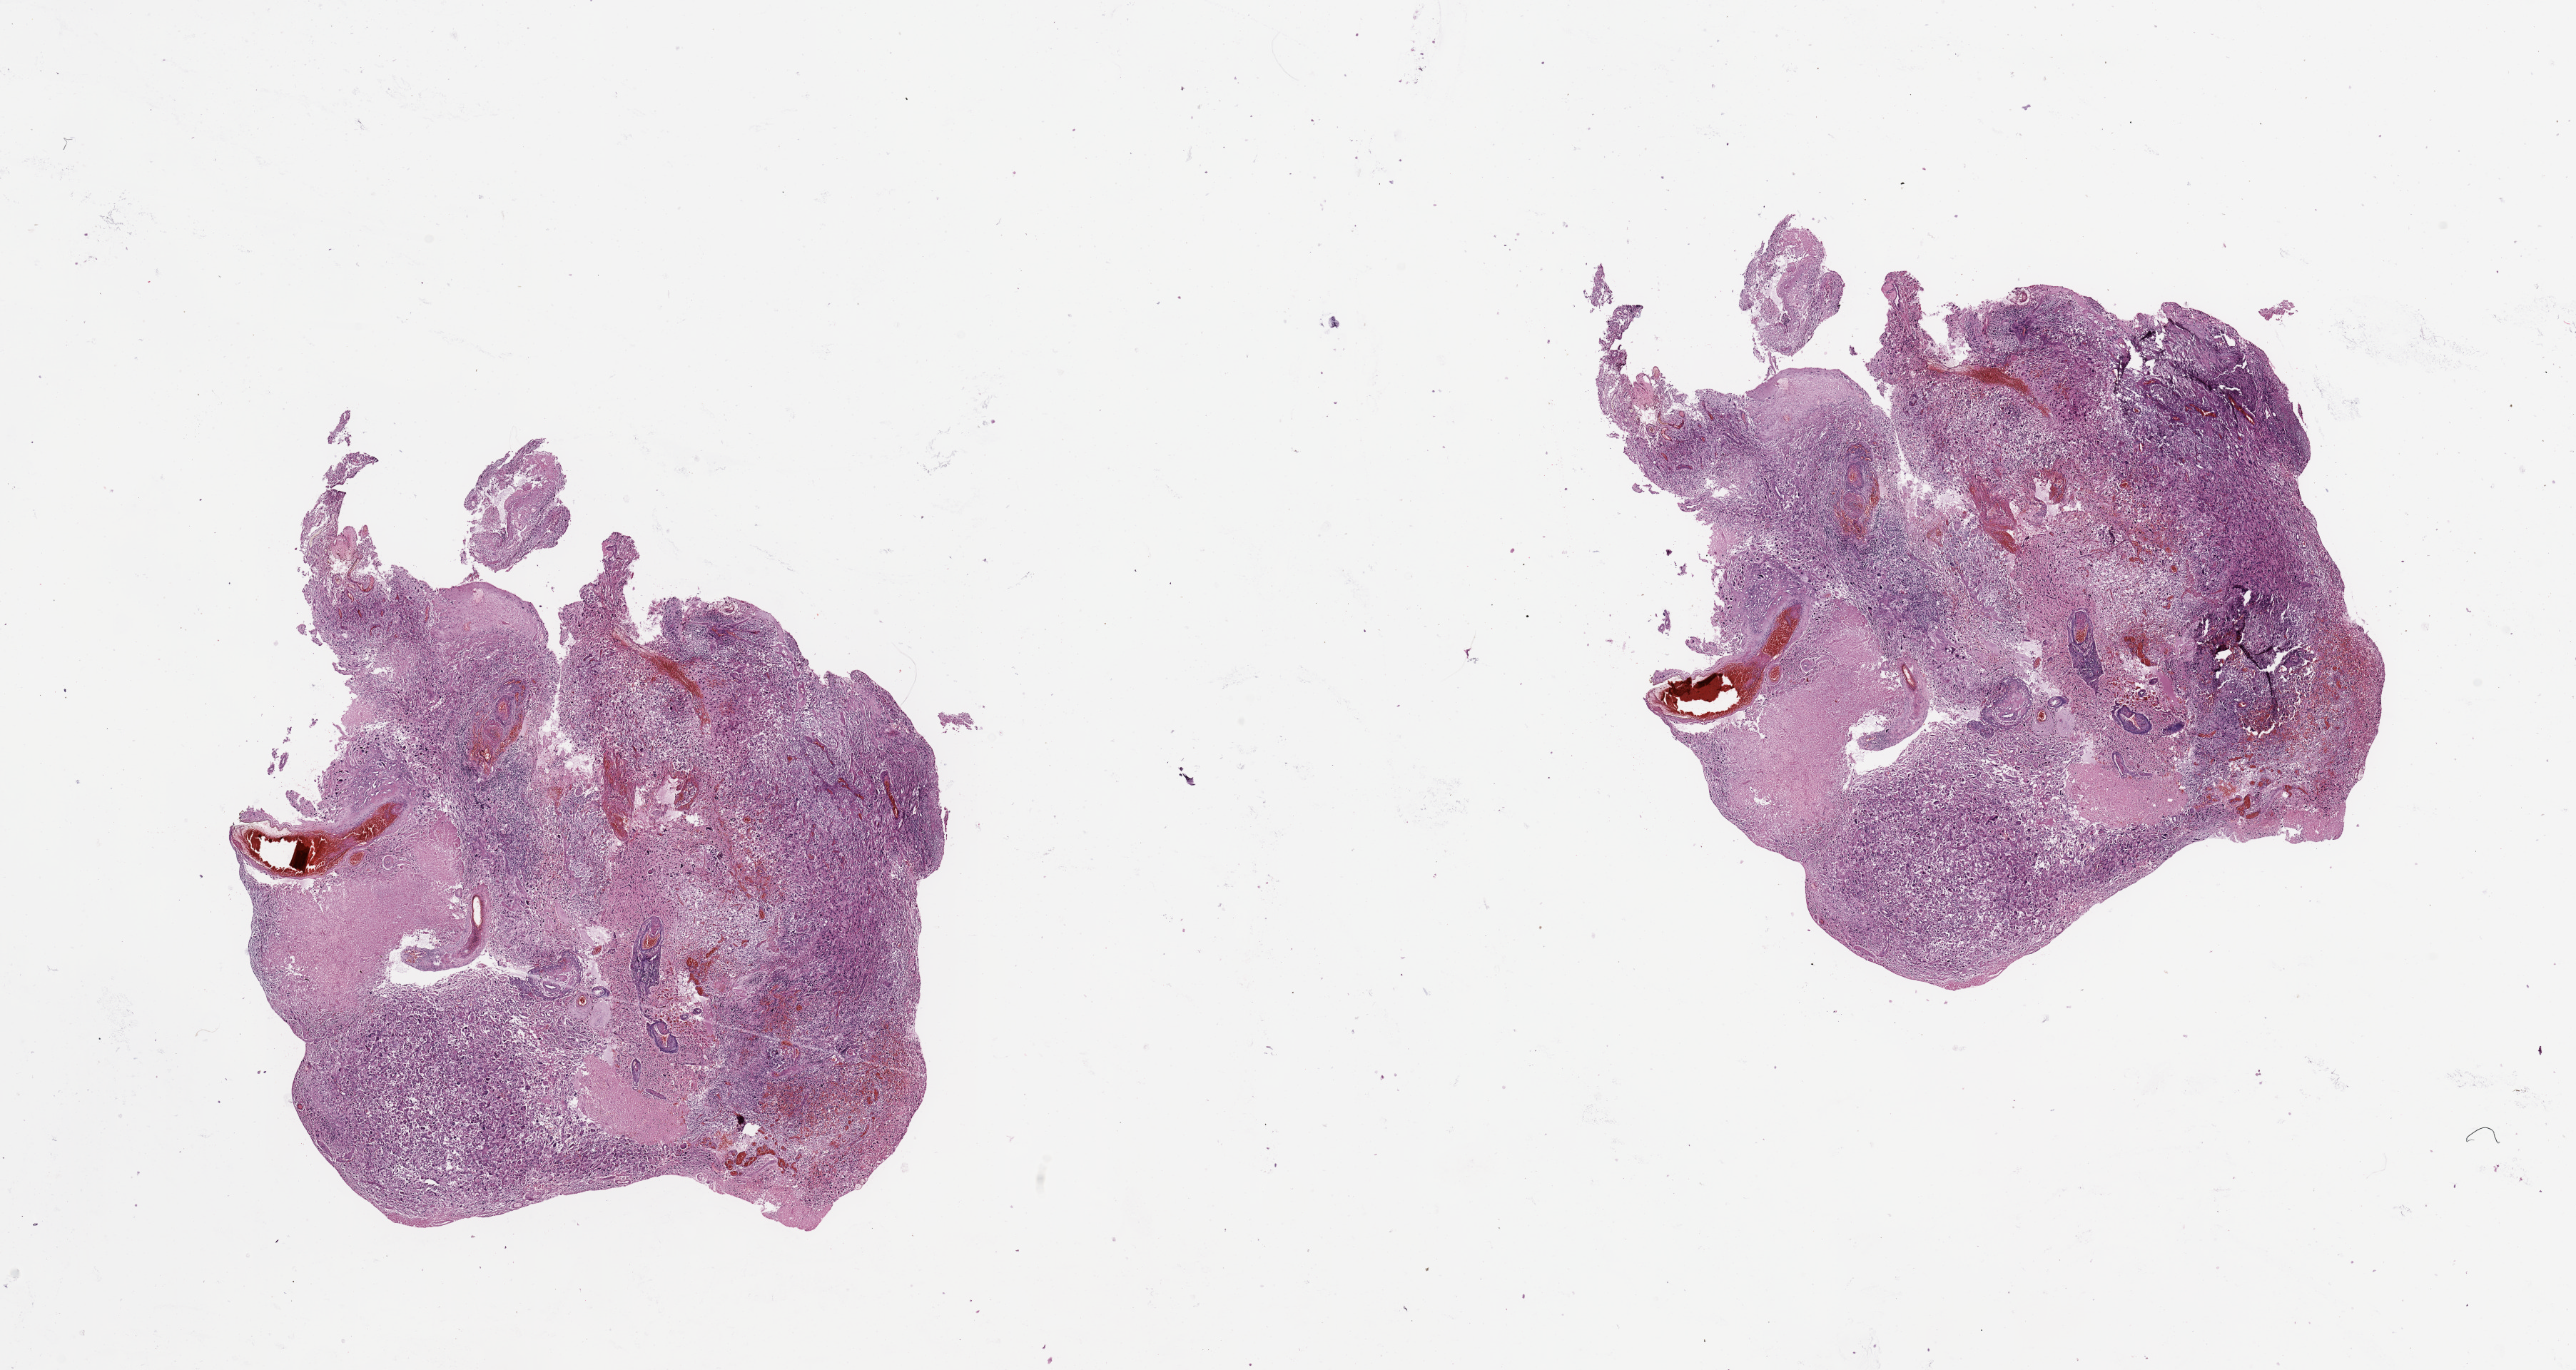
Whole-slide histology image, Hematoxylin and eosin (H&E) stained, shown as a low-resolution overview of the whole scanned area (about 28.5 x 15.2 mm, slide scanned at 20x), tumour tissue sample, brain. Male, 77 y/o.
Histologic diagnosis: Glioblastoma. Primary tumour site (as recorded): frontal lobe.